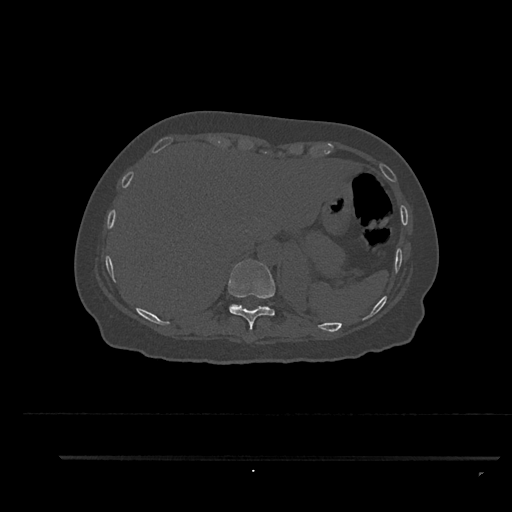
CT including the spine, one axial slice; position 357 of 797 along the scan axis; reconstruction kernel Br40s/3; 120 kVp; bone window (W 1800 / L 400 HU); 0.5 mm slice thickness; 512 × 512 image matrix. Female patient, age 44 years. From the clinical record (not read from this slice): primary cancer: renal.
Annotated regions visible in this slice (semi-automatic segmentation, software-assisted and operator-edited):
- T10 vertebra: box from (x=228, y=259) to (x=275, y=332) px